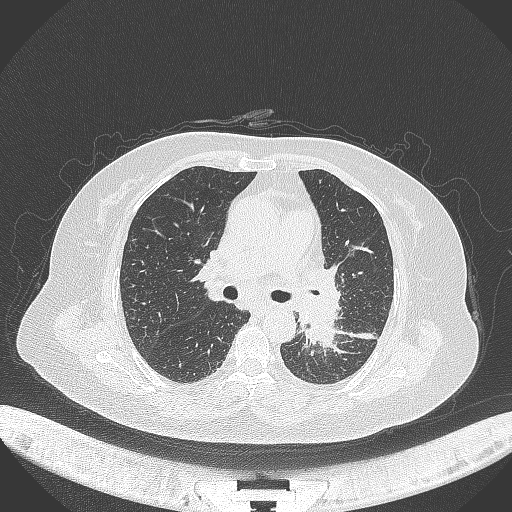
Chest CT, one axial slice. Position 207 of 322 along the scan axis. Lung window (W 1500 / L -600 HU). 1 mm slice thickness. 512 × 512 image matrix, field of view 400 × 400 mm. Female patient, age 69 years. Case-level facts recorded for this patient, not image findings: clinical TNM (as recorded): T2b N3 M1.
Annotated regions visible in this slice (bounding box drawn by a radiologist):
- lung tumour (recorded histology: adenocarcinoma): box from (x=297, y=310) to (x=341, y=349) px